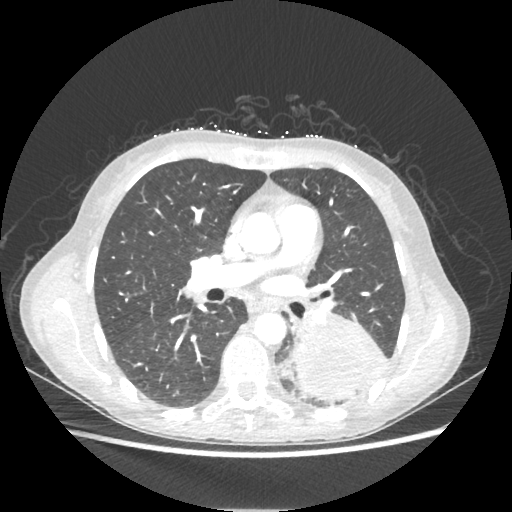
Chest CT, one axial slice. Position 120 of 221 along the scan axis. Reconstruction kernel STANDARD. Lung window (W 1500 / L -600 HU). 1.25 mm slice thickness. 512 × 512 image matrix, field of view 360 × 360 mm. Patient: female, 53 years. Case-level facts recorded for this patient, not image findings: clinical TNM (as recorded): T3 N0 M0.
Structures marked on this image (rectangle marked by the reading radiologist):
- lung tumour (recorded histology: adenocarcinoma): bounding box [x1, y1, x2, y2] px = [293, 302, 387, 402]